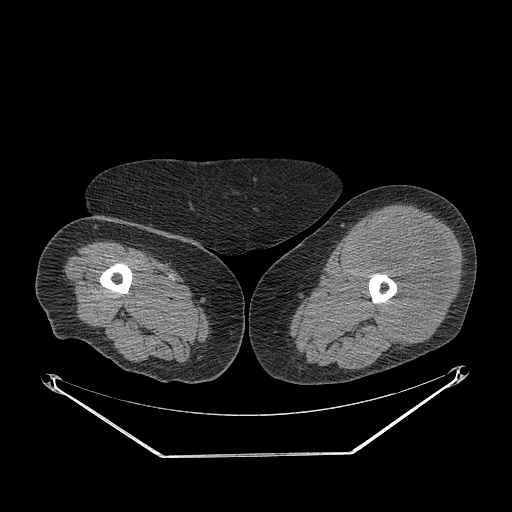
CT of an extremity soft-tissue mass (from a PET/CT study), one axial slice. Position 228 of 267 along the scan axis. Soft-tissue window (W 400 / L 40 HU). 512 × 512 image matrix, field of view 500 × 500 mm. Female patient. From the clinical record (not read from this slice): histological type: undifferentiated – high grade; grade: high; site of the primary tumour: left thigh.
Annotated regions visible in this slice (expert contour drawn on MRI and transferred to this co-registered scan by the dataset authors):
- gross tumour volume including surrounding oedema: box from (x=354, y=215) to (x=453, y=344) px
- gross tumour volume (mass): (x=354, y=215)–(x=453, y=344)